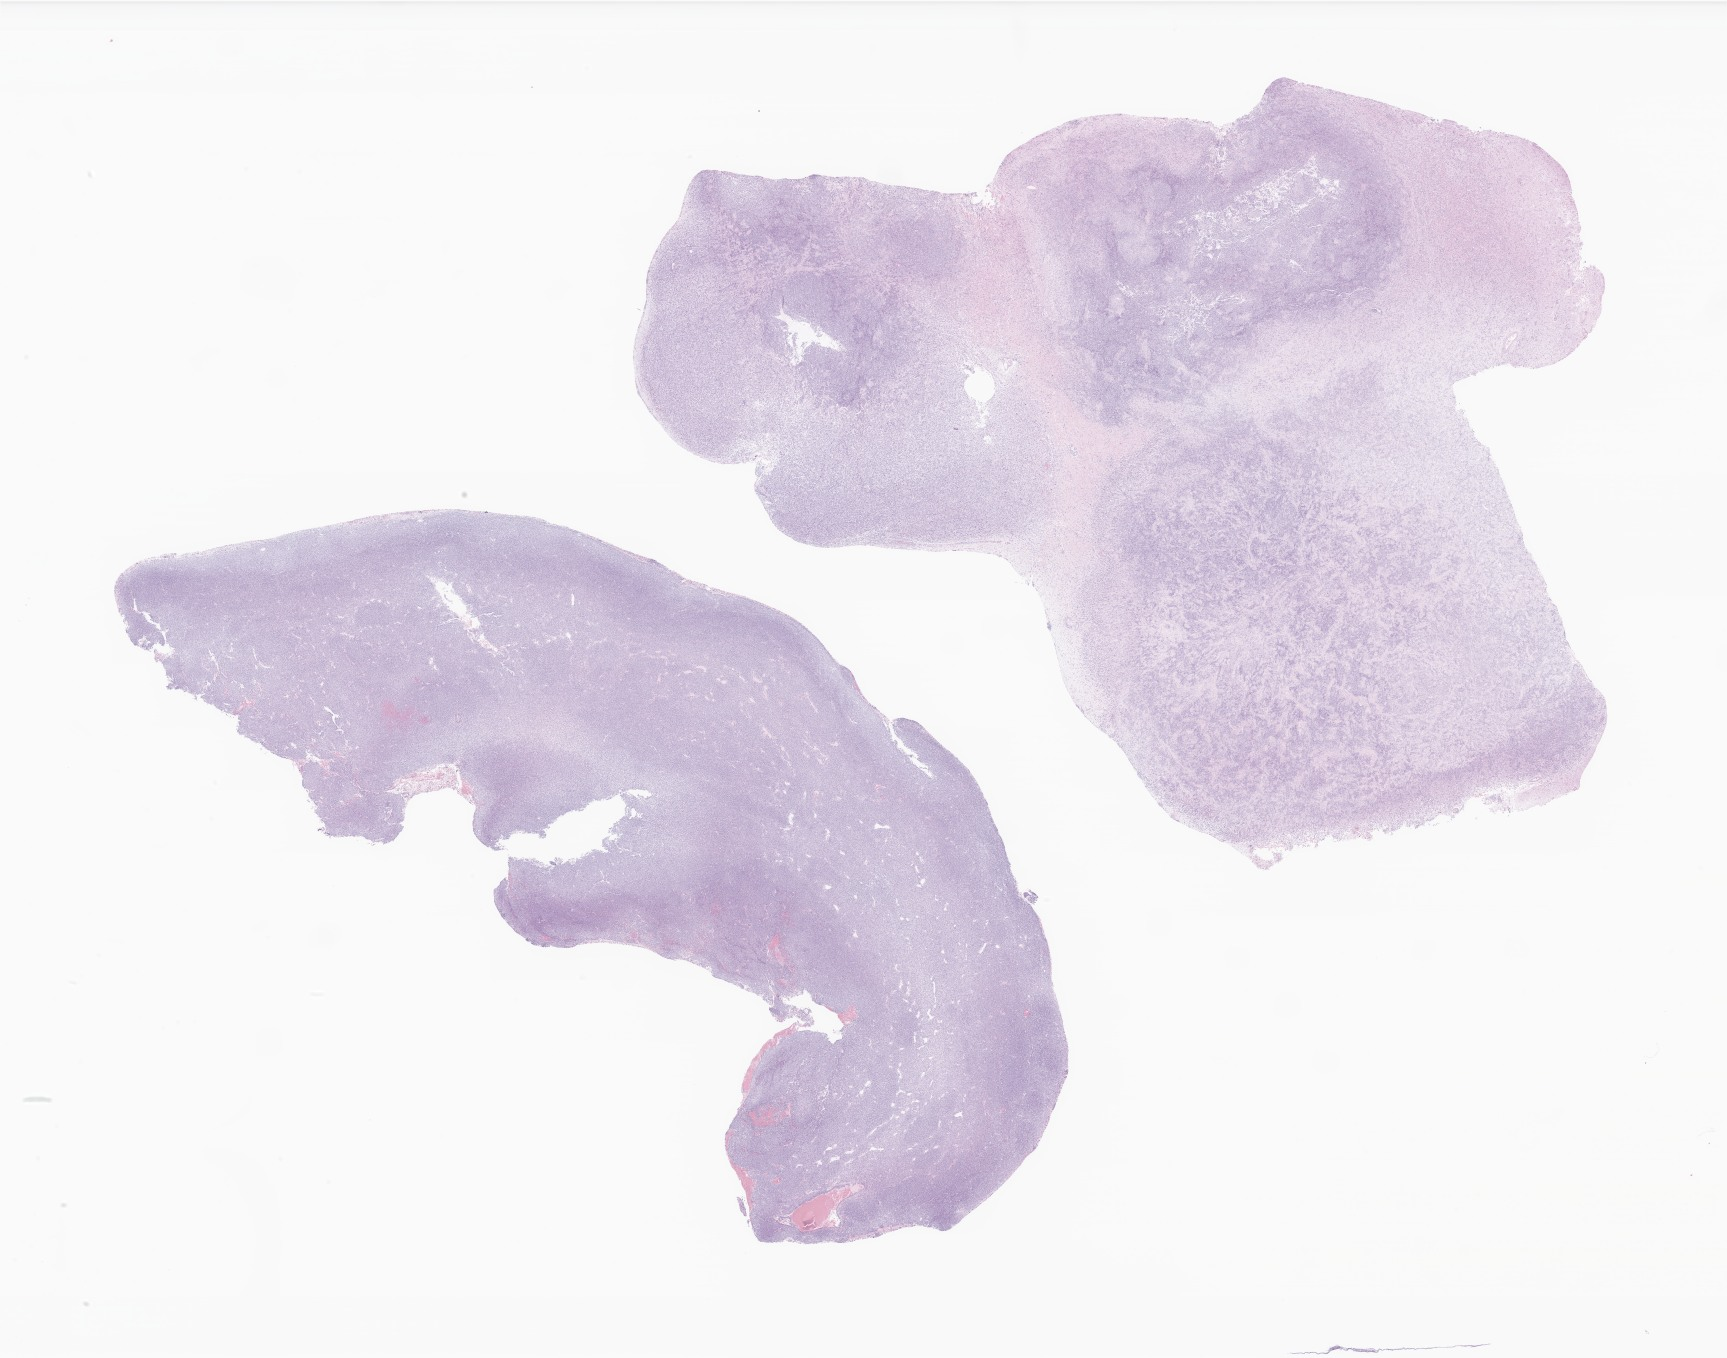
Haematoxylin and eosin whole-slide image of tumor tissue from the brain — whole scanned area (about 29.1 x 22.9 mm) shown as a low-resolution overview. Formalin-fixed paraffin-embedded section. Patient male; age 69 months (5 years 9 months).
Diagnosis (ICD-O-3 morphology term): Glioma, malignant.